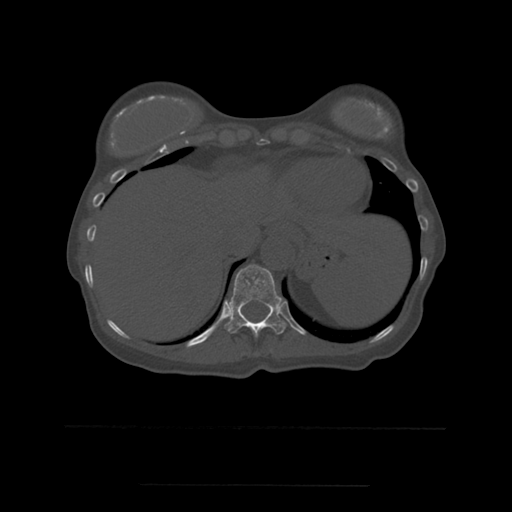
CT including the spine, one axial slice; slice 284 of 544 in the series (ordered by position); bone window (W 1800 / L 400 HU); 1.25 mm slice thickness; 512 × 512 image matrix. Patient age 58 years. From the clinical record (not read from this slice): primary cancer: lung.
Structures marked on this image (semi-automatically segmented with operator editing):
- T11 vertebra: box from (x=225, y=265) to (x=287, y=337) px